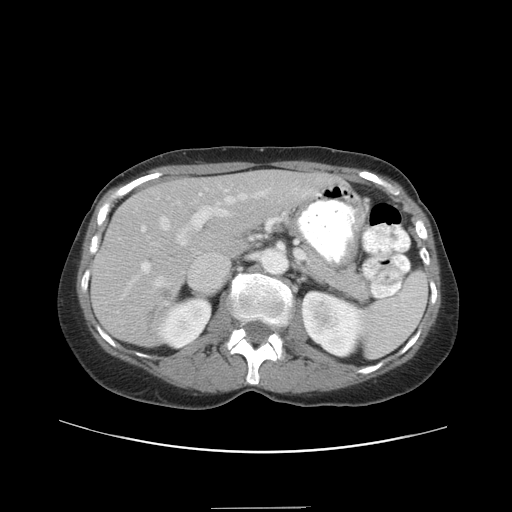
Contrast-enhanced abdominal CT, one axial slice; position 23 of 38 along the scan axis; 120 kVp; intravenous contrast given; soft-tissue window (W 400 / L 40 HU); 512 × 512 image matrix, field of view 388 × 388 mm. Female patient, age 64 years. From the clinical record (not read from this slice): diagnosis: colorectal cancer liver metastases, imaged before liver resection; multiple liver metastases: no; largest metastasis: 3.8 cm; disease in both lobes: yes.
Annotated regions visible in this slice (outlined manually by an expert reader):
- hepatic veins: bounding box <152,191,266,288> (left, top, right, bottom; pixels)
- liver: <94,171,329,345>
- planned liver remnant (the part of the liver to remain after resection): <135,171,329,255>
- portal vein (with intrahepatic branches): <141,189,229,273>